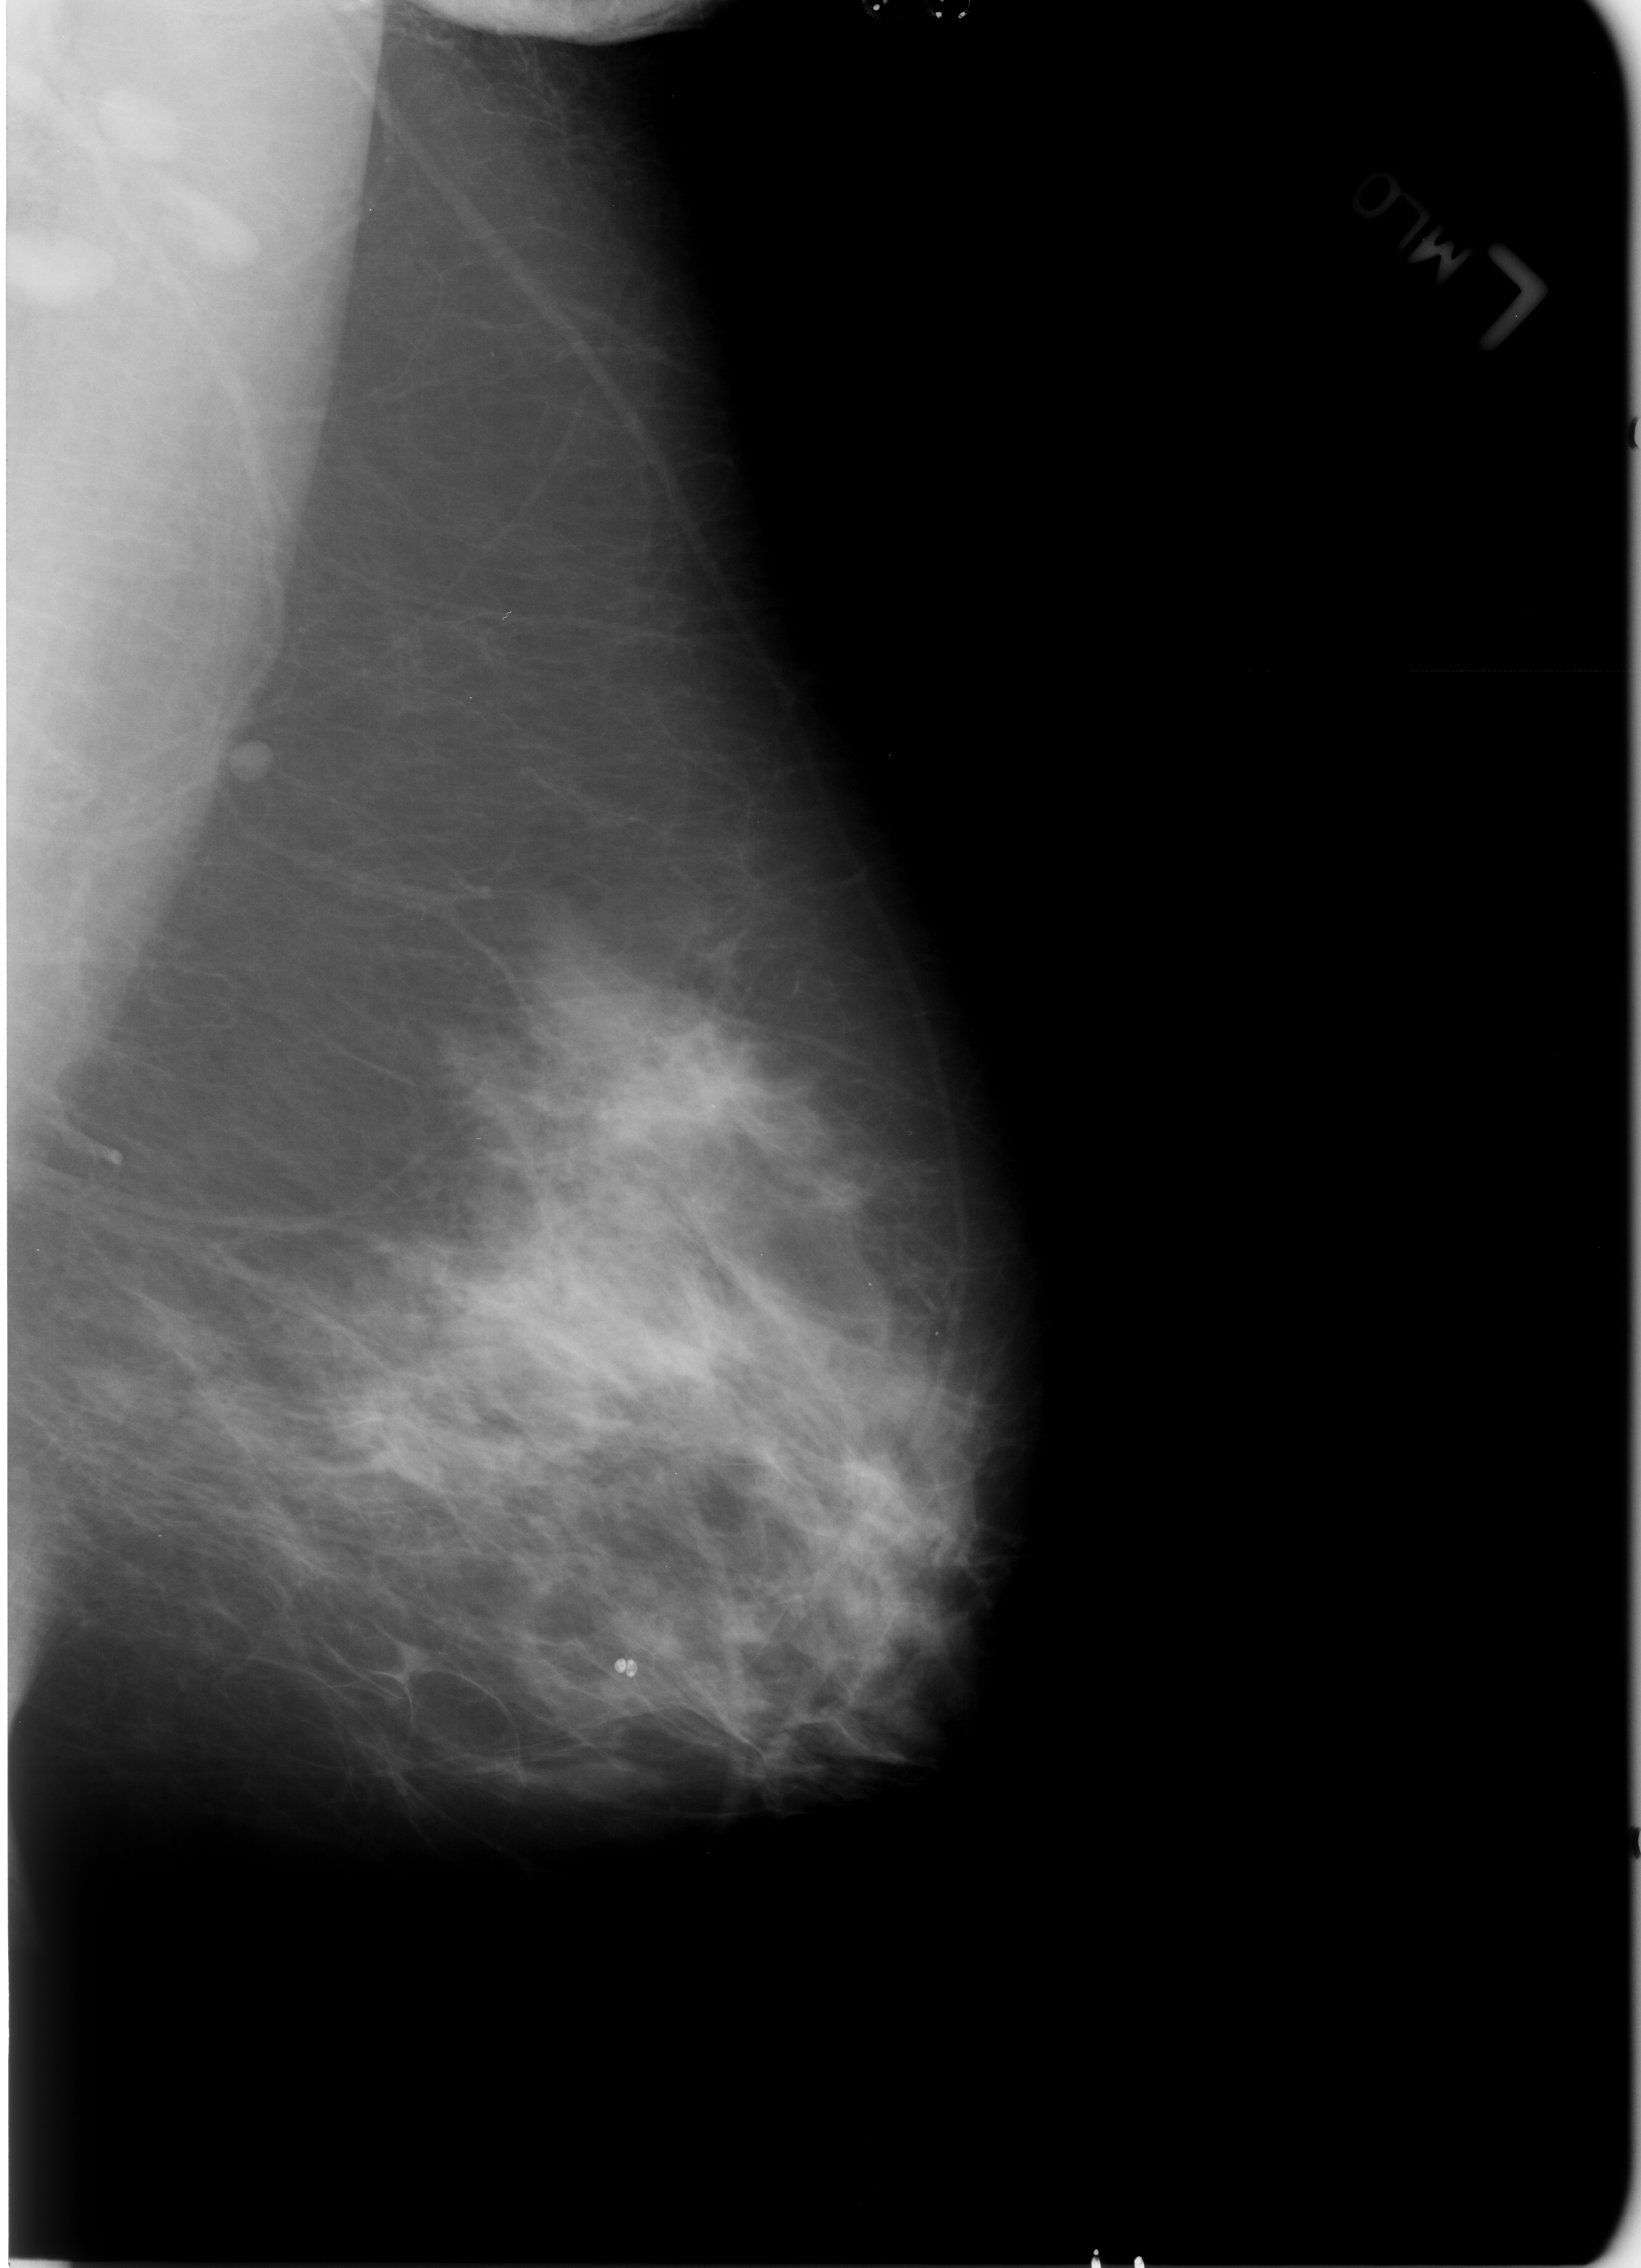
Digitized screen-film mammogram, left breast, mediolateral oblique (MLO) view.
Marked findings (only marked abnormalities are described; nothing is implied about the rest of the image): calcifications, morphology lucent center; BI-RADS assessment category 2; benign without callback (not worked up further).